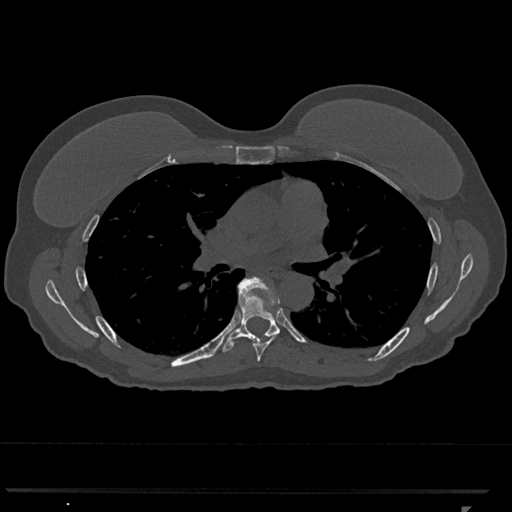
CT including the spine, one axial slice. Bone window (W 1800 / L 400 HU). 0.5 mm slice thickness. 512 × 512 image matrix, field of view 380 × 380 mm. Female patient, age 62 years. From the clinical record (not read from this slice): primary cancer: renal.
Annotated regions visible in this slice (semi-automatic segmentation, software-assisted and operator-edited):
- T6 vertebra: bounding box <238,281,280,362> (left, top, right, bottom; pixels)
- T7 vertebra: <218,276,281,352>